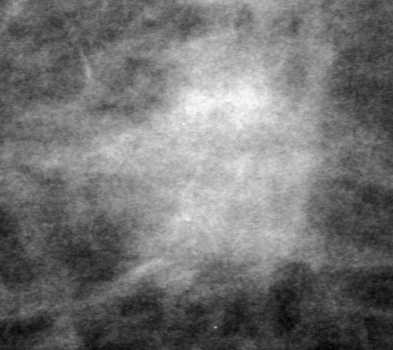
Region of interest cut from a scanned film mammogram (one marked finding), left breast, CC view, BI-RADS breast density category 2 (scale 1–4).
- Mass, shape oval, margins obscured; BI-RADS assessment category 4; subtlety rating 4 on a 1 (subtle) to 5 (obvious) scale; pathology result (as recorded, not read from the image): malignant.